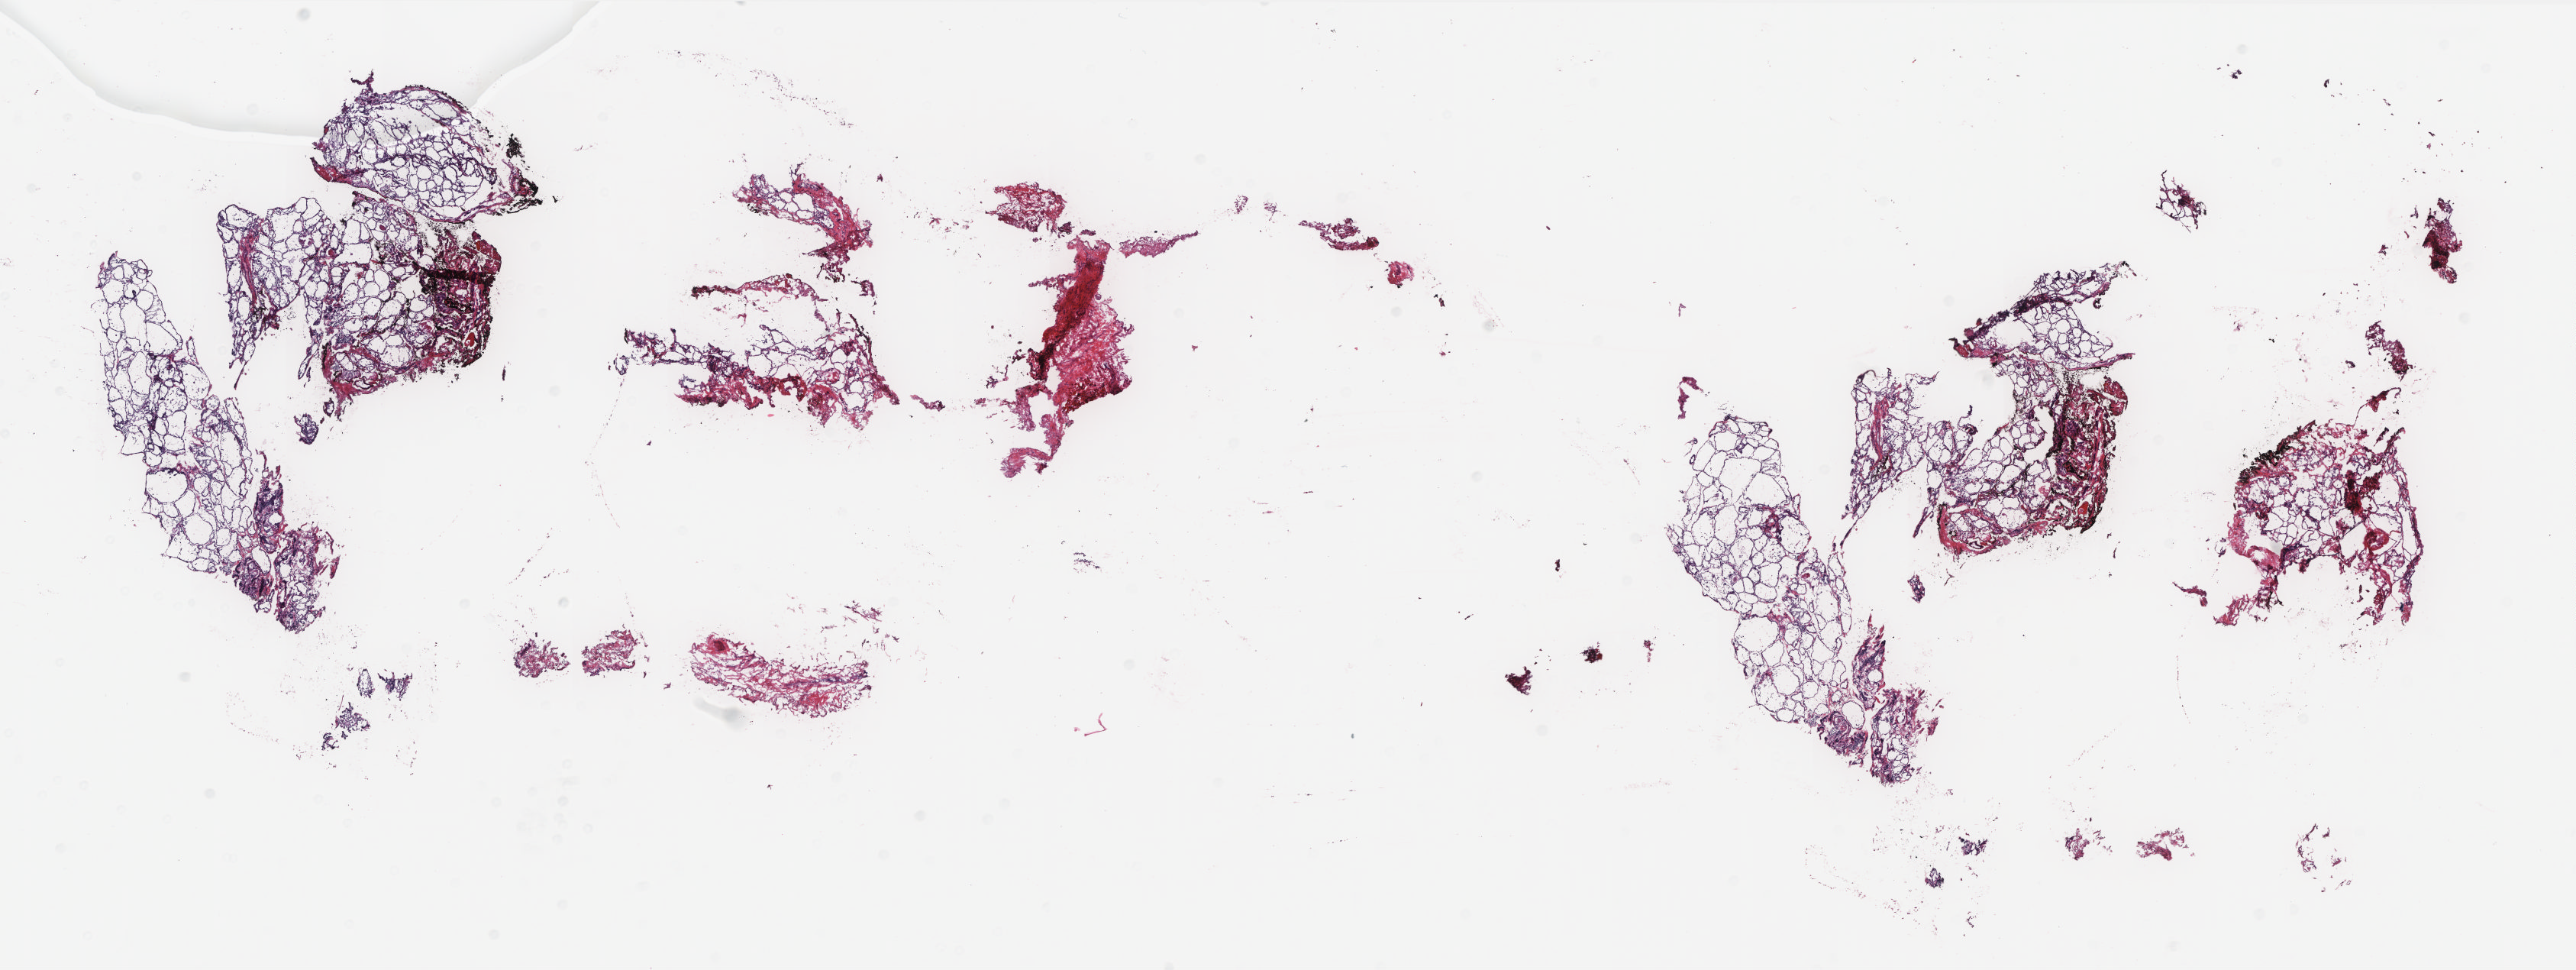
Whole-slide histology image, H&E — low-resolution overview of the scanned area, about 26.9 x 10.1 mm, frozen section from the top of the tissue portion, sample: solid tissue normal (non-tumour tissue), thyroid. Female, age 30 years at initial diagnosis. Composition of this section per pathologist review: tumour cells 0%, tumour nuclei 0%, normal cells 100%, stromal cells 0%, necrosis 0%. Inflammatory infiltration, as recorded: lymphocyte infiltration 10%, monocyte infiltration 0%, neutrophil infiltration 0%.
• this section: solid tissue normal sample (biorepository sample class)
• patient diagnosis: Papillary adenocarcinoma, NOS (thyroid gland)